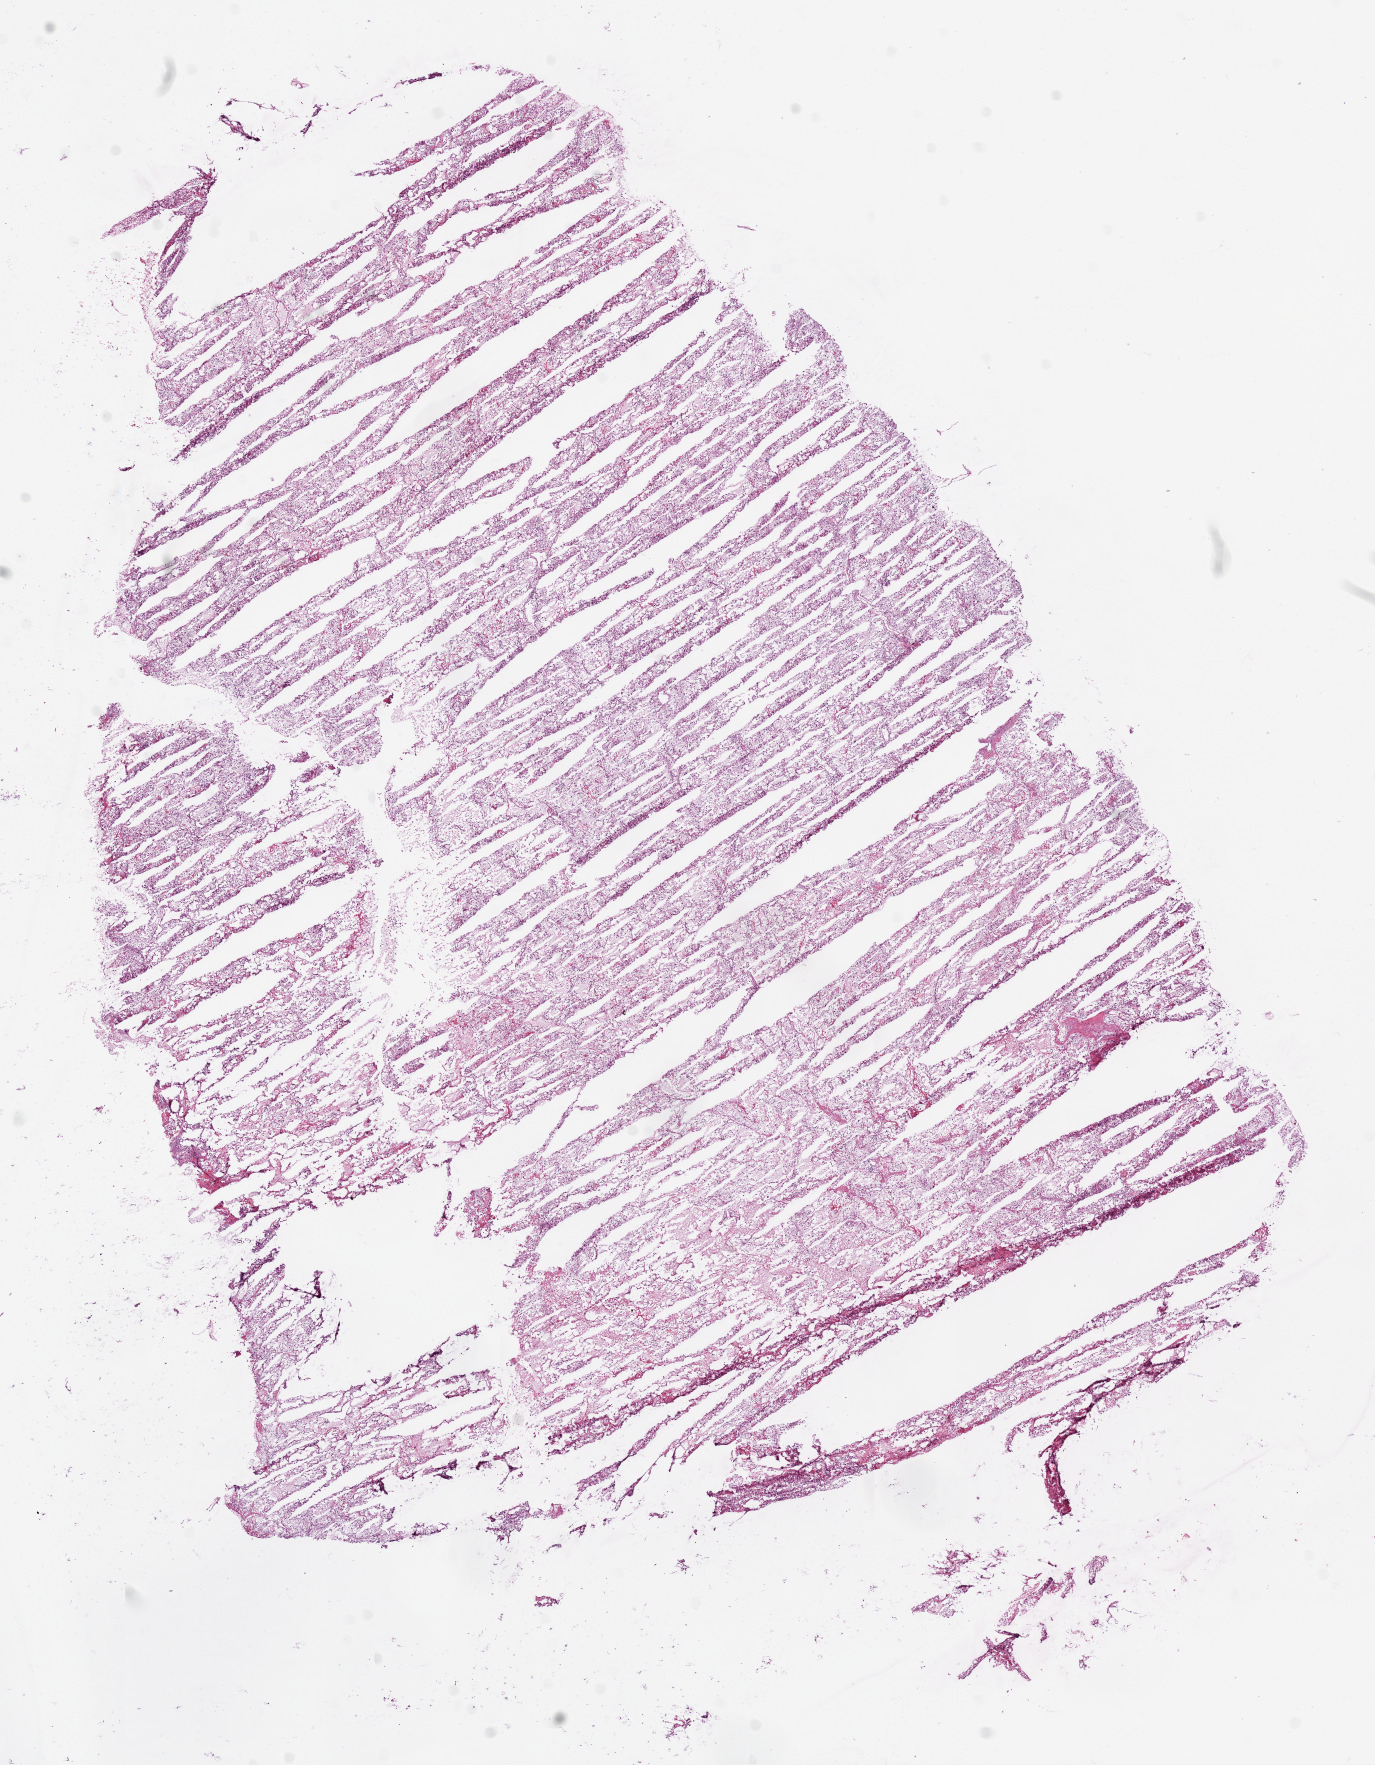
Whole-slide histology image, H&E-stained, whole scanned area (about 11.0 x 14.2 mm) shown as a low-resolution overview, frozen section, kidney, primary tumour sample. Male, age 49 years at initial diagnosis. Histologic grade: G3 (poorly differentiated). Pathologist review of this section (percent, as recorded): tumour cells 95%, tumour nuclei 90%, normal cells 0%, stromal cells 5%, necrosis 0%.
- lymph nodes positive (case pathology): 0 of 3 examined
- AJCC pathologic stage: II
- diagnosis: Clear cell adenocarcinoma, NOS